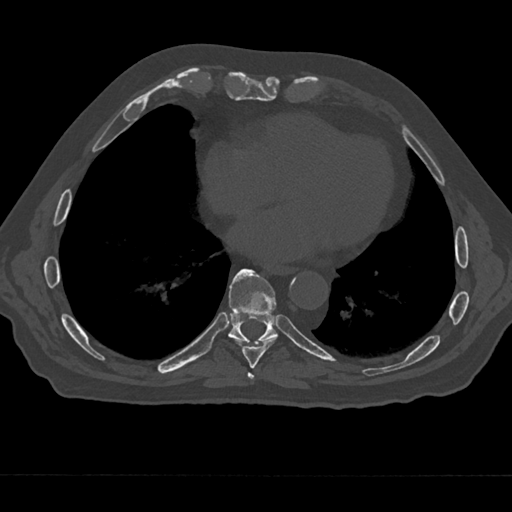
CT including the spine, one axial slice. Slice 290 of 797 in the series (ordered by position). Reconstruction kernel Br40s/3. Bone window (W 1800 / L 400 HU). 0.5 mm slice thickness. 512 × 512 image matrix, field of view 377 × 377 mm. Patient: male, 75 years. From the clinical record (not read from this slice): primary cancer: renal; vertebrae with lytic lesions (as recorded): T4.
Annotated regions visible in this slice (semi-automatically segmented with operator editing):
- T7 vertebra: box from (x=247, y=372) to (x=255, y=384) px
- T8 vertebra: (x=234, y=313)–(x=277, y=368)
- T9 vertebra: (x=228, y=268)–(x=277, y=343)